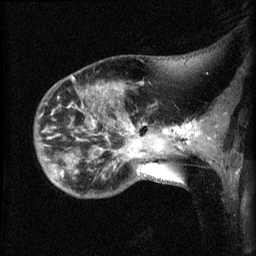
Breast MRI (dynamic contrast-enhanced), one sagittal slice; slice 17 of 60 in the series (ordered by position); dynamic contrast-enhanced series, image 2 of 3 at this slice position (ordered by acquisition); 1.5 T; TE 4.2 ms, TR 8.2 ms; 2.1 mm slice thickness; 256 × 256 image matrix, field of view 180 × 180 mm. Patient: female, 50 years.
Structures marked on this image (semi-automatically segmented with operator editing):
- analysis volume of interest (the breast-tissue region the enhancement analysis was run in; not a lesion): bounding box [x1, y1, x2, y2] px = [38, 81, 169, 198]
- tumour enhancement mask (voxels above the 70 % enhancement threshold inside the analysis volume of interest): [130, 126, 169, 134]